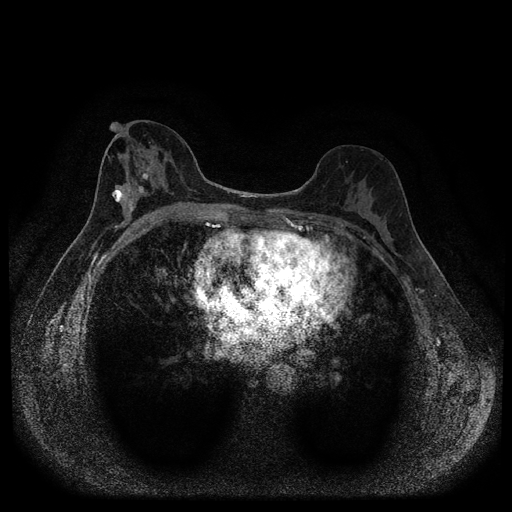
Breast MRI (dynamic contrast-enhanced, multi-phase), one axial slice. Slice 51 of 116 in the series (ordered by position). Dynamic contrast-enhanced series, time point 2 of 5 at this slice position (early post-contrast). 1.5 T. TE 2.7 ms, TR 5.4 ms. 2 mm slice thickness. 512 × 512 image matrix, field of view 330 × 330 mm. Patient: female, 49 years.
Outlined on this slice (semi-automatically segmented with operator editing):
- breast lesion (labelled 'tumour' in the annotation; benign lesions carry a separate 'benign' label): bounding box <111,188,127,203> (left, top, right, bottom; pixels)